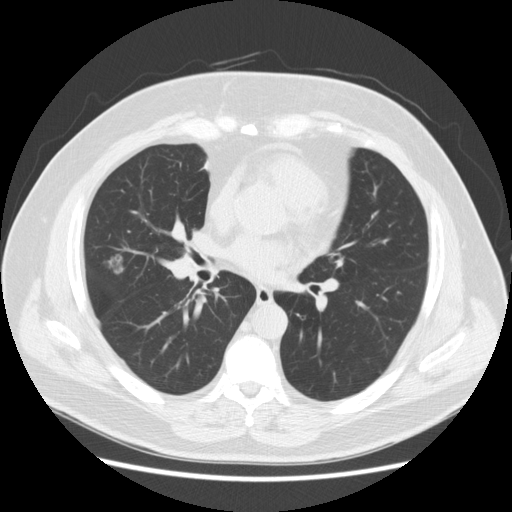
Axial slice from a low-dose chest CT screening exam; first (baseline) screen; lung window (W 1500 / L -600 HU); 2.5 mm slice thickness; 512 × 512 image matrix. Male participant, aged 67 years at enrolment. Former smoker at enrolment.
- Lesion marked by an expert reader, bounding box <91,250,132,290> (left, top, right, bottom; pixels).
- Reader record for this screening exam (exam-level; its link to the box is not recorded): non-calcified nodule or mass ≥4 mm, right middle lobe, 15 × 11 mm, smooth margins, soft tissue attenuation.
- Lung cancer was diagnosed 409 days after this screen (after the second annual screen): adenocarcinoma, NOS, right middle lobe, moderately differentiated (G2), stage IA (AJCC 6th edition), 14 mm at pathology.